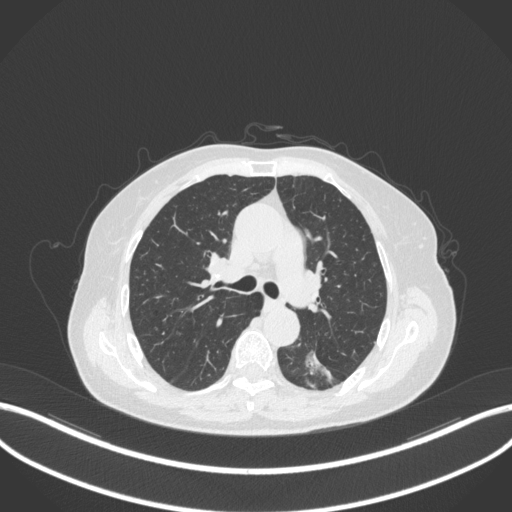
Chest CT, one axial slice. Lung window (W 1500 / L -600 HU). 1 mm slice thickness. 512 × 512 image matrix, field of view 400 × 400 mm. Female patient, age 70 years. Case-level facts recorded for this patient, not image findings: clinical TNM (as recorded): T1c N0 M0.
Structures marked on this image (bounding box drawn by a radiologist):
- lung tumour (recorded histology: adenocarcinoma): bounding box <294,345,333,389> (left, top, right, bottom; pixels)